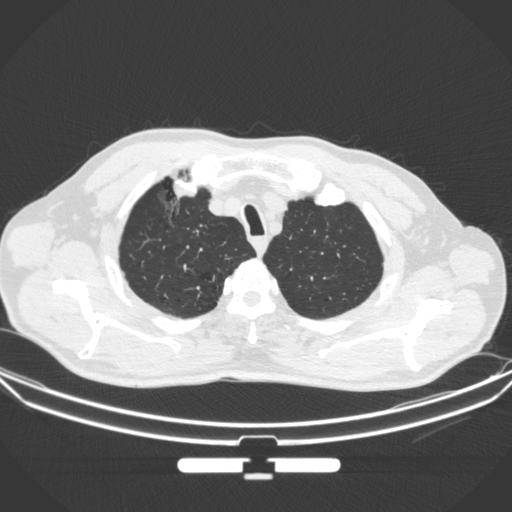
Chest CT, one axial slice; position 296 of 355 along the scan axis; lung window (W 1500 / L -600 HU); 1 mm slice thickness; 512 × 512 image matrix, field of view 399 × 399 mm. Patient: male, 67 years. From the clinical record (not read from this slice): clinical TNM (as recorded): T1c N0 M0; histopathological grade: G2.
Outlined on this slice (bounding box drawn by a radiologist):
- lung tumour (recorded histology: adenocarcinoma): bounding box <148,182,201,236> (left, top, right, bottom; pixels)